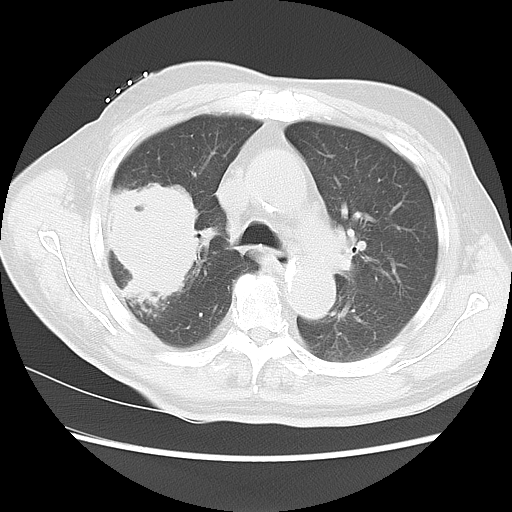
Chest CT, one axial slice; position 10 of 15 along the scan axis; 120 kVp; lung window (W 1500 / L -600 HU); 5 mm slice thickness; 512 × 512 image matrix, field of view 350 × 350 mm. Patient: male, 68 years. From the clinical record (not read from this slice): clinical TNM (as recorded): T4 N3 M0.
Annotated regions visible in this slice (rectangle marked by the reading radiologist):
- lung tumour (recorded histology: squamous cell carcinoma): bounding box <102,178,198,302> (left, top, right, bottom; pixels)